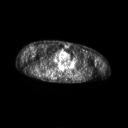
FDG PET of an extremity soft-tissue mass (from a PET/CT study), one axial slice; position 178 of 267 along the scan axis; 128 × 128 image matrix. Patient: male, 61 years. From the clinical record (not read from this slice): histological type: pleiomorphic spindle cell undifferentiated; grade: high; site of the primary tumour: right parascapusular.
Structures marked on this image (expert contour drawn on MRI and transferred to this co-registered scan by the dataset authors):
- gross tumour volume including surrounding oedema: bounding box <35,70,59,78> (left, top, right, bottom; pixels)